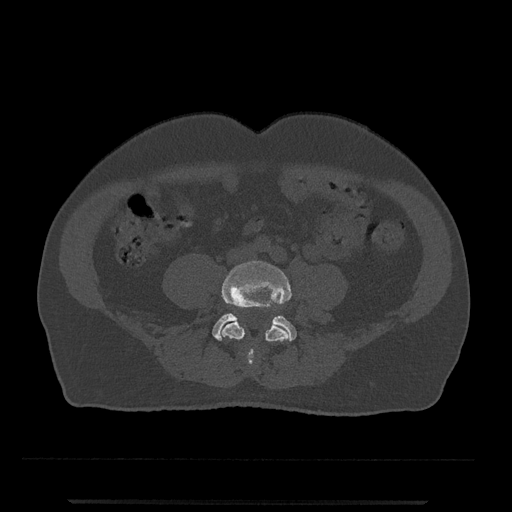
CT including the spine, one axial slice. Slice 108 of 797 in the series (ordered by position). Bone window (W 1800 / L 400 HU). 0.5 mm slice thickness. 512 × 512 image matrix, field of view 419 × 419 mm. Patient: male, 63 years. Case-level facts recorded for this patient, not image findings: primary cancer: prostate.
Annotated regions visible in this slice (semi-automatic segmentation, software-assisted and operator-edited):
- L4 vertebra: bounding box (x1, y1, x2, y2) in pixels: (220, 261, 292, 365)
- L5 vertebra: (212, 313, 297, 341)